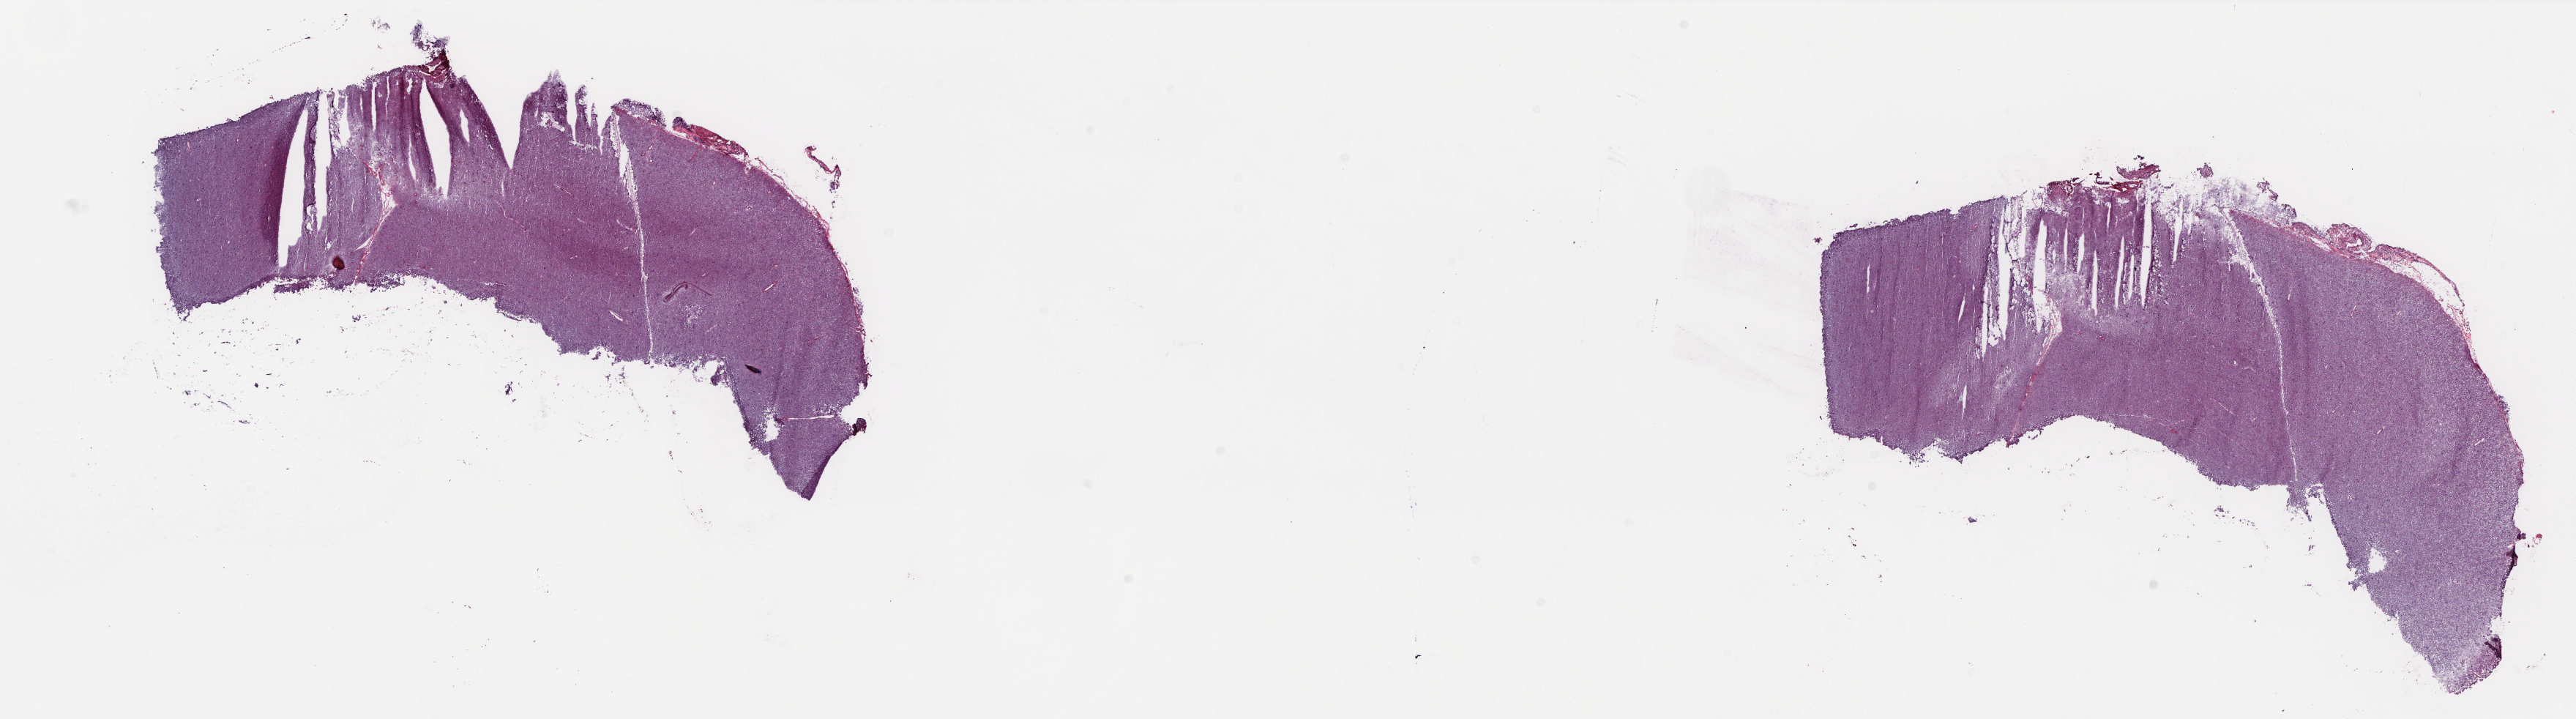
Digitized H&E tissue section (whole slide), a low-resolution overview of the entire scanned area, about 28.4 x 7.9 mm (slide scanned at 20x), frozen section, sample: solid tissue normal (non-tumour tissue), brain.
This section: solid tissue normal sample (biorepository sample class).